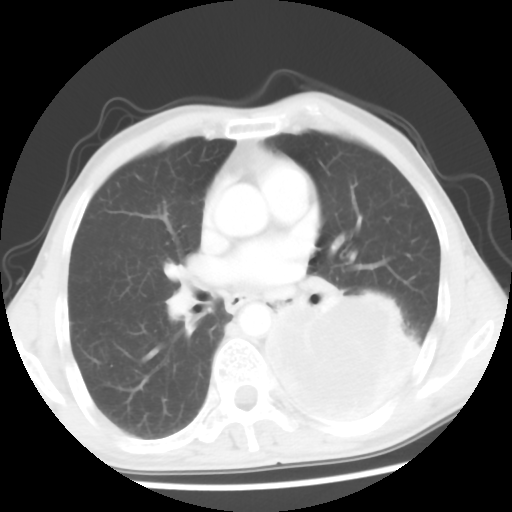
Chest CT, one axial slice; slice 30 of 56 in the series (ordered by position); lung window (W 1500 / L -600 HU); 5 mm slice thickness; 512 × 512 image matrix. Male patient, age 60 years. From the clinical record (not read from this slice): clinical TNM (as recorded): T4 N0 M0.
Outlined on this slice (bounding box drawn by a radiologist):
- lung tumour (recorded histology: squamous cell carcinoma): bounding box <257,292,418,433> (left, top, right, bottom; pixels)